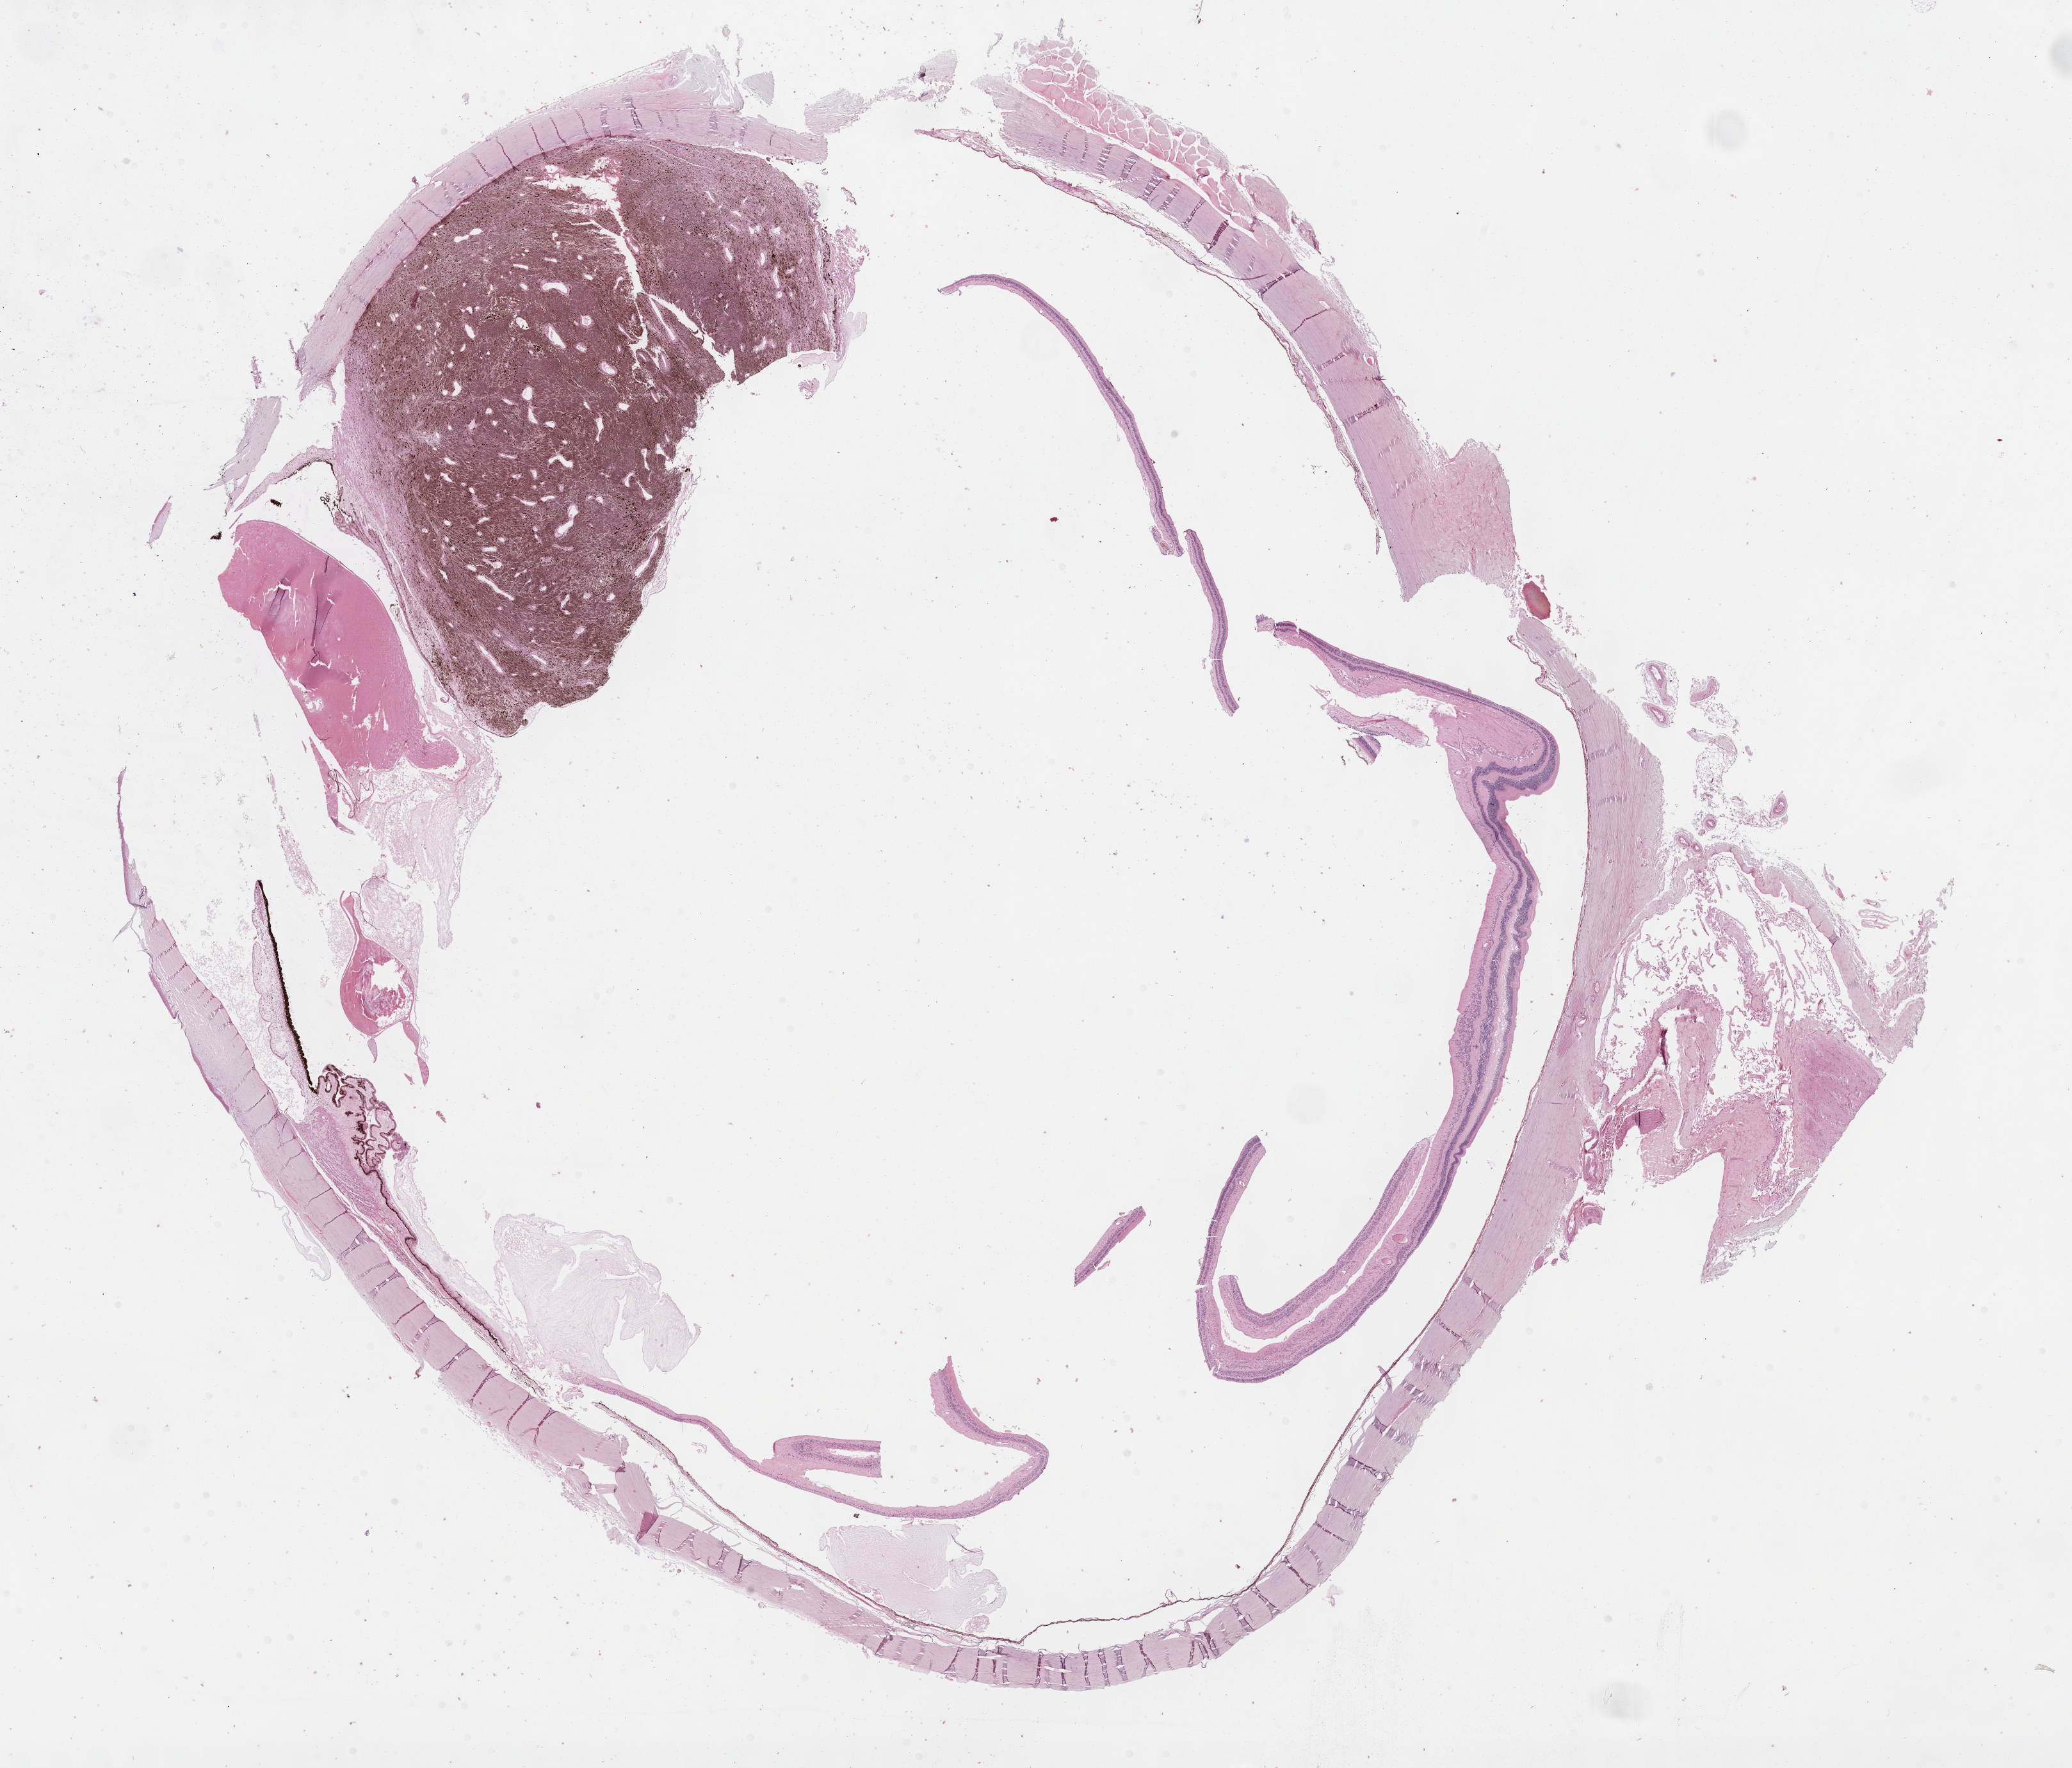
Whole-slide histology image, Hematoxylin and eosin (H&E) stained, shown as a low-resolution overview of the whole scanned area (about 26.2 x 22.3 mm). Formalin-fixed paraffin-embedded (FFPE) diagnostic section. Primary tumour sample from the uvea. Patient: female, age at initial diagnosis 78 years.
* TNM: T3b N0 M0
* pathologic diagnosis: Spindle cell melanoma, NOS (ciliary body)
* AJCC pathologic stage: IIIA